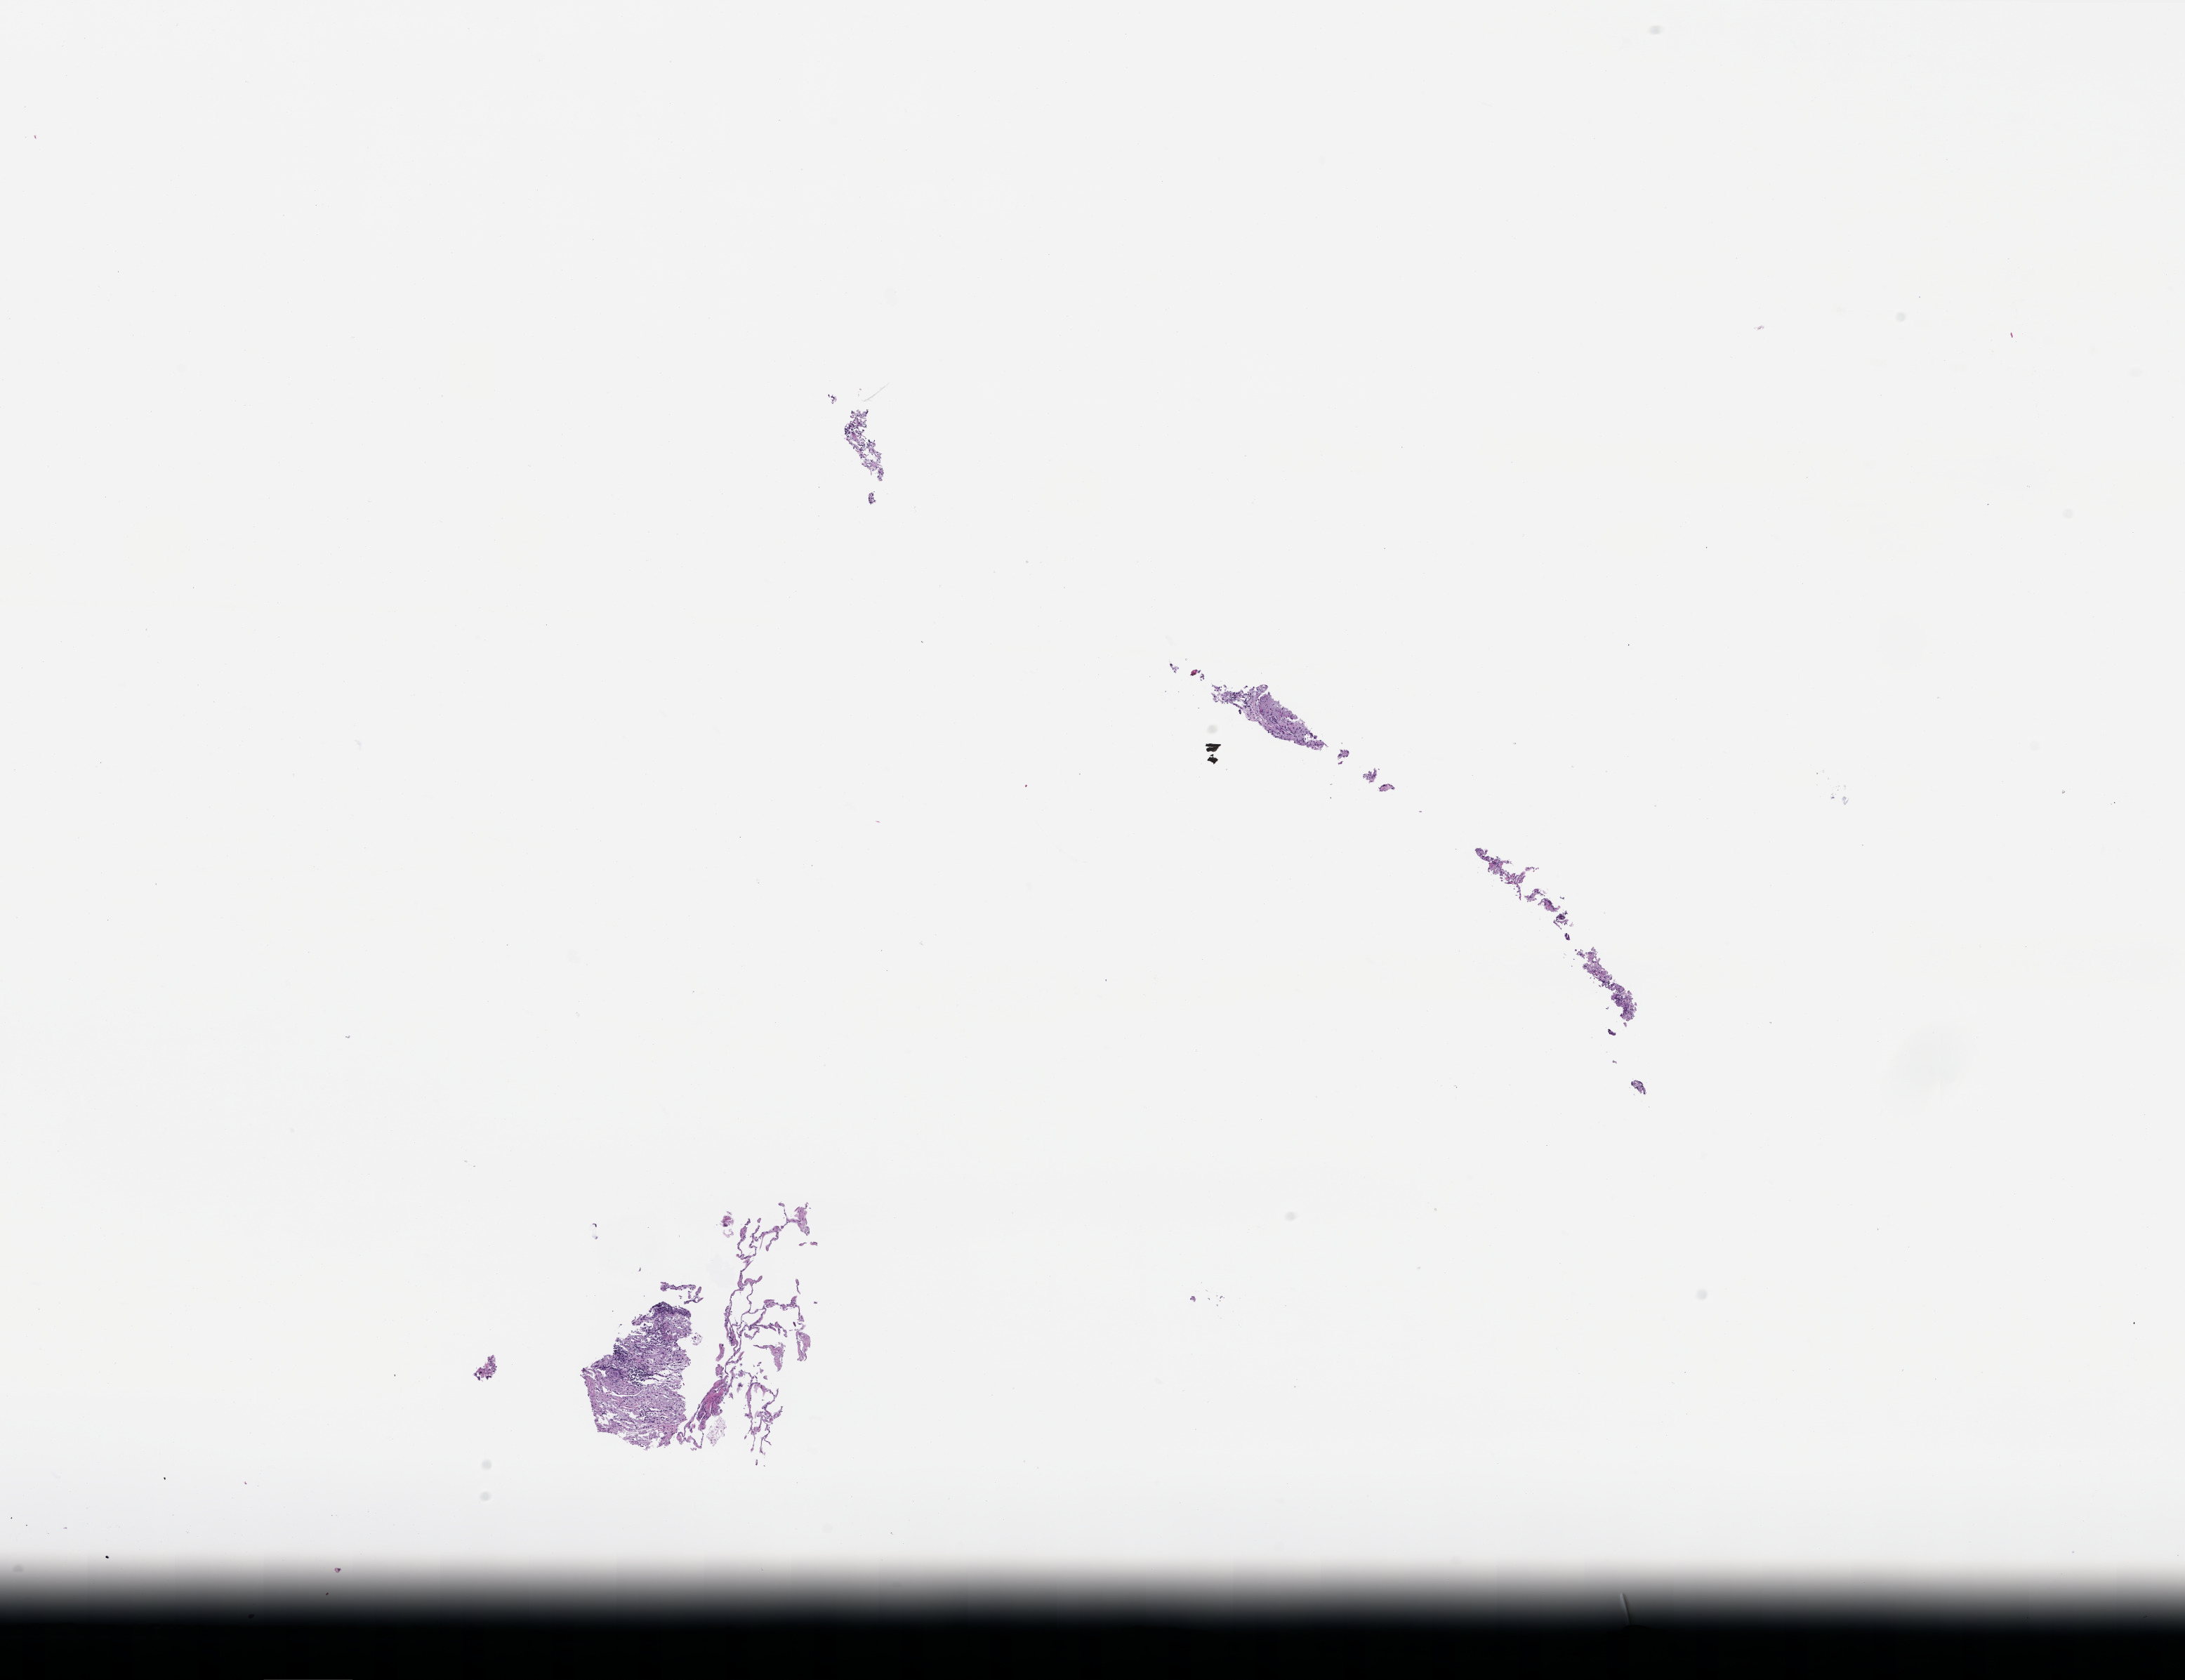
H&E whole-slide image, low-resolution overview of the scanned area, about 12.6 x 9.7 mm. FFPE section. Tissue site: lung. Specimen time point: archival tissue. Patient: female.
This section: primary tumour tissue. Diagnosis: Non-Small Cell Lung Carcinoma.